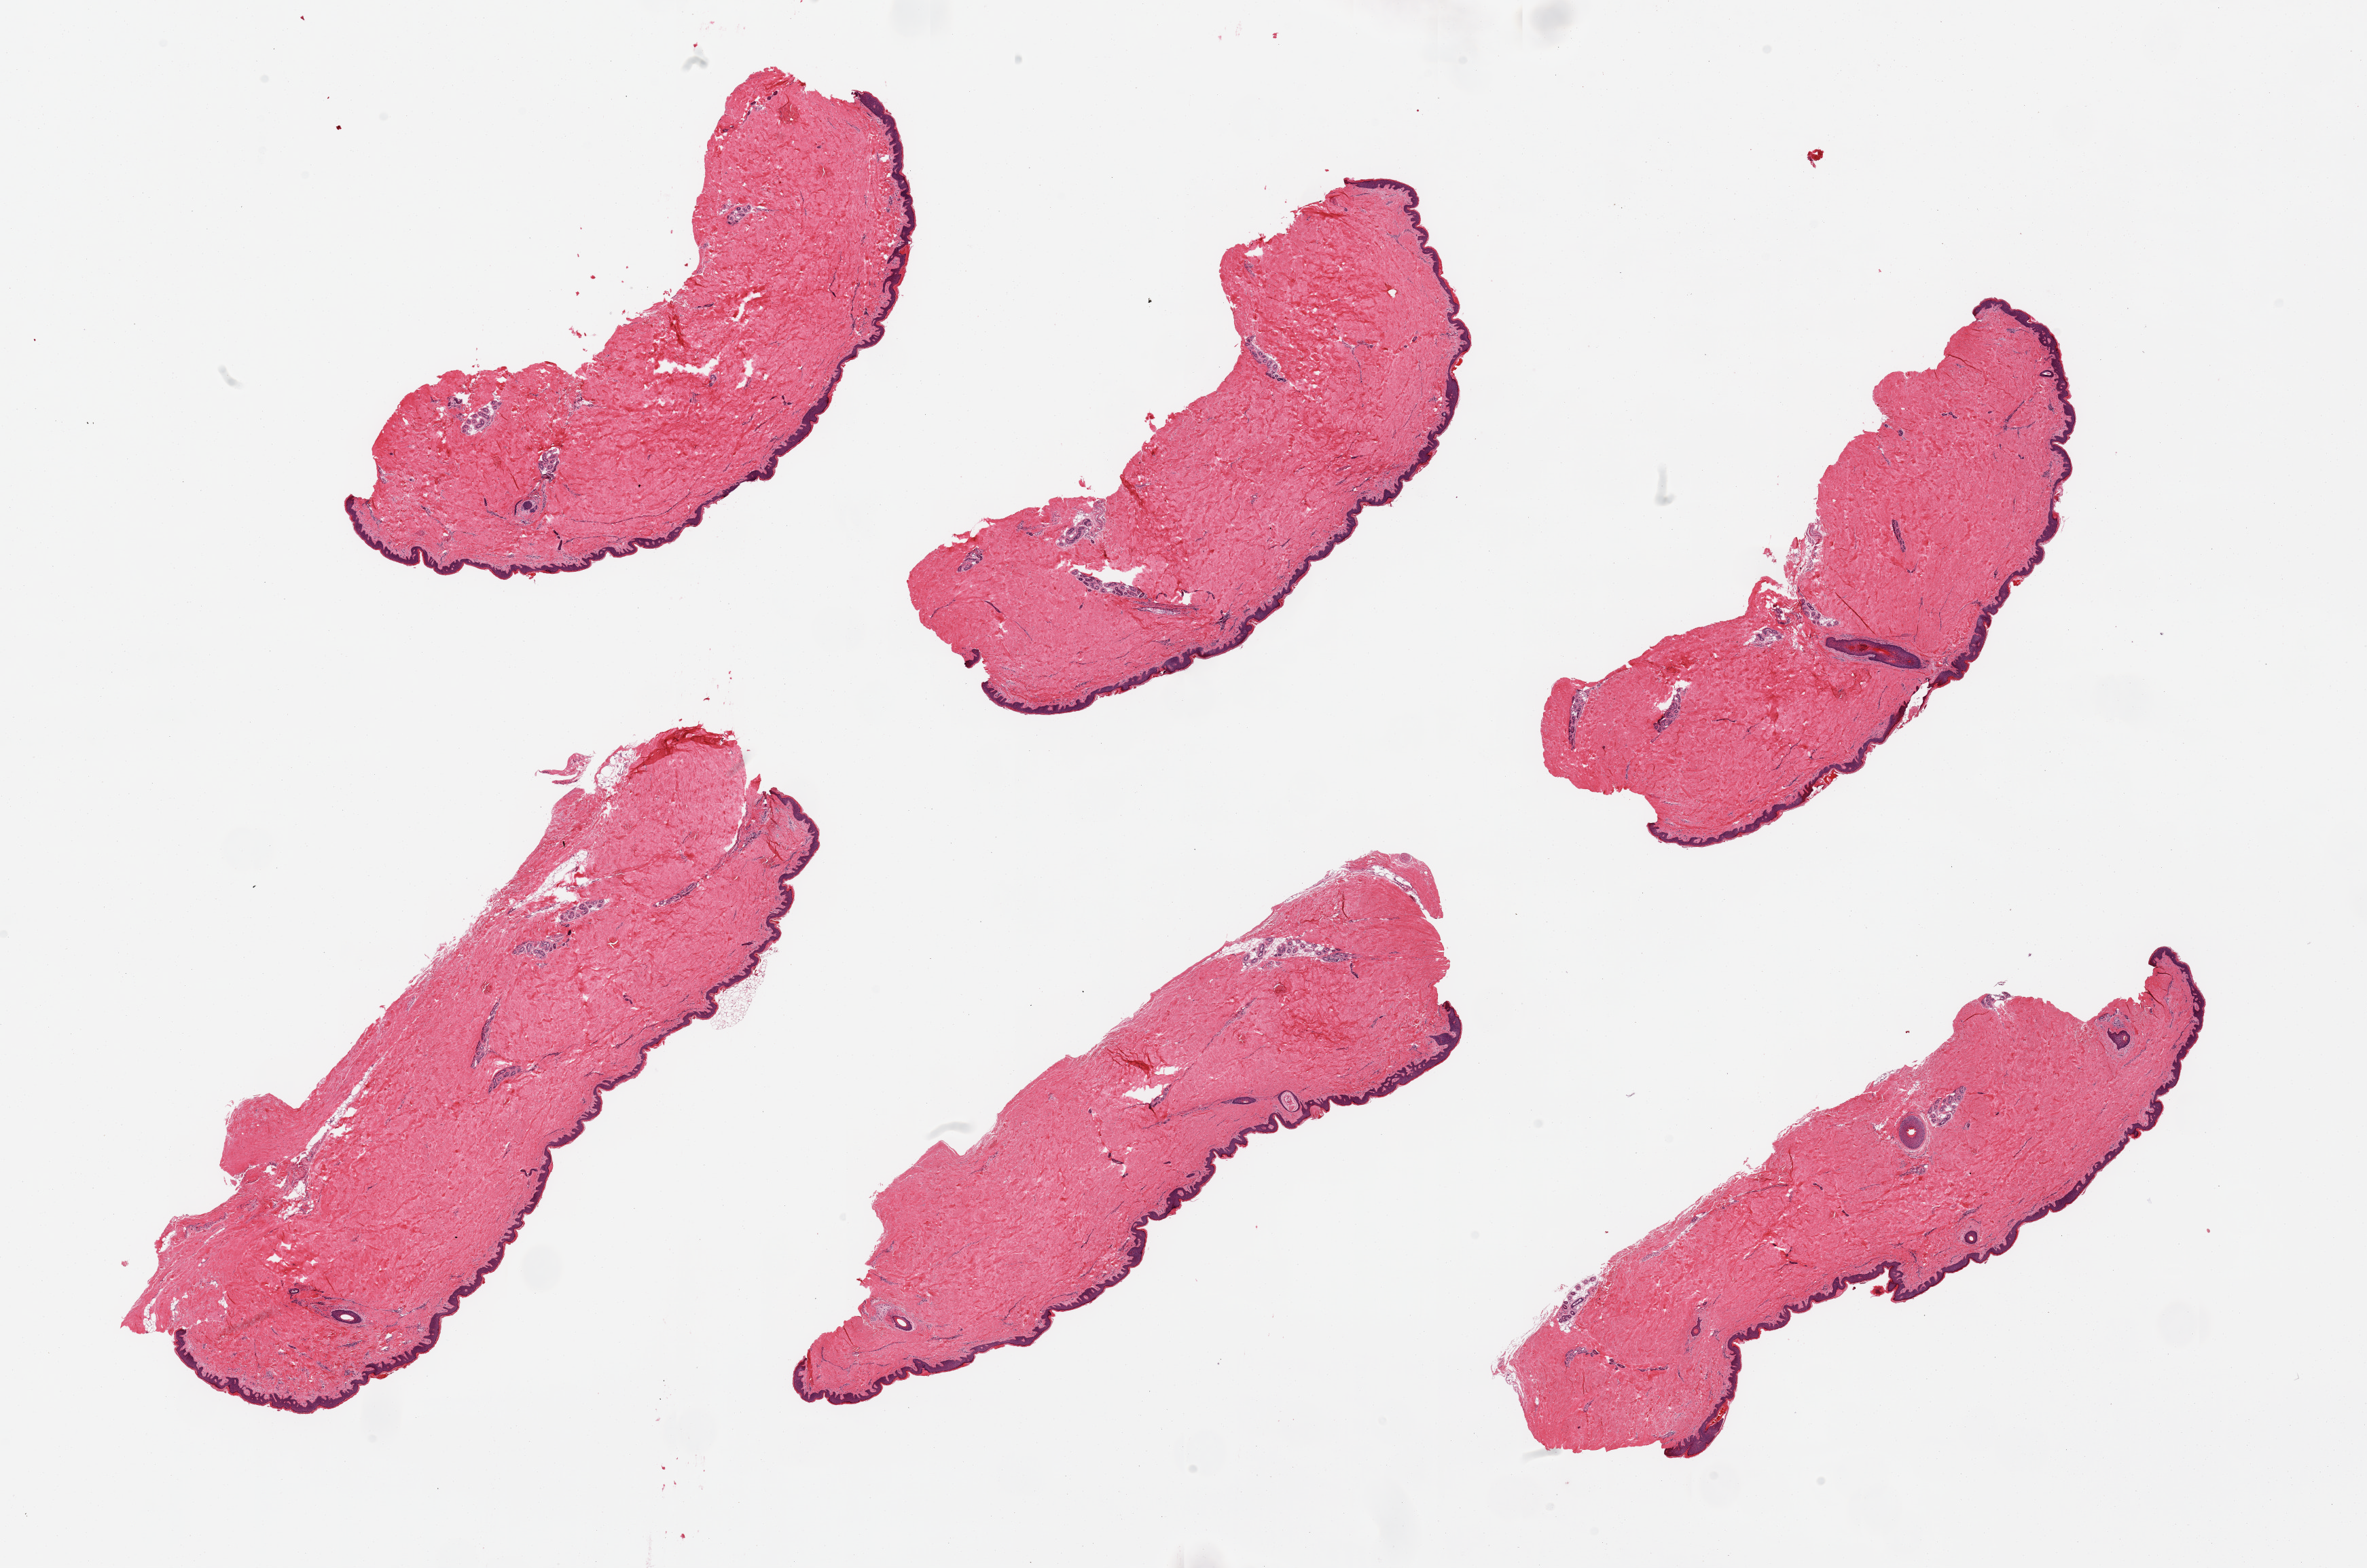
Digitized H&E-stained section — low-resolution overview of the scanned area, about 27.6 x 18.3 mm, PAXgene-fixed, paraffin-embedded tissue, section of skin of suprapubic region (target tissue), donor tissue sample. Donor: male.
Pathologist's review note for this sample: 6 pieces, no dermal fat; squamous epithelium is ~40 microns.